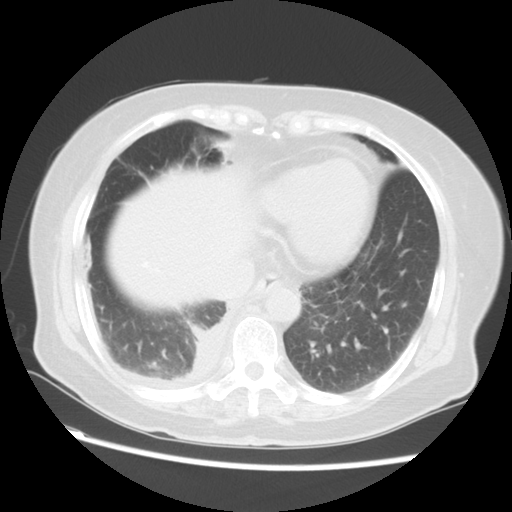
Chest CT, one axial slice; position 20 of 57 along the scan axis; 120 kVp; lung window (W 1500 / L -600 HU); 5 mm slice thickness; 512 × 512 image matrix, field of view 350 × 350 mm. Patient: female, 69 years. From the clinical record (not read from this slice): clinical TNM (as recorded): T2 N1 M1a.
Structures marked on this image (rectangle marked by the reading radiologist):
- lung tumour (recorded histology: adenocarcinoma): bounding box (x1, y1, x2, y2) in pixels: (187, 319, 227, 395)